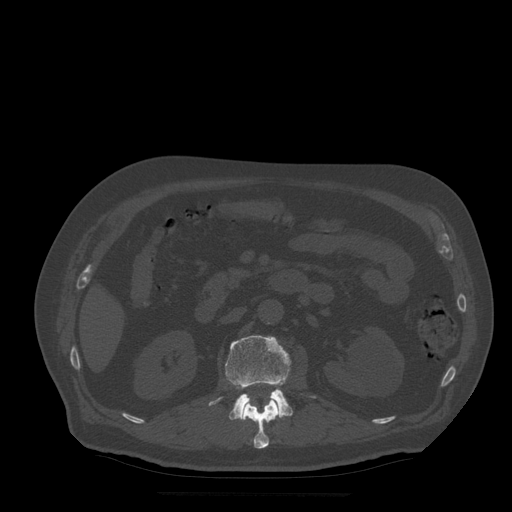
CT including the spine, one axial slice; slice 180 of 522 in the series (ordered by position); bone window (W 1800 / L 400 HU); 1.25 mm slice thickness; 512 × 512 image matrix, field of view 420 × 420 mm. Patient age 72 years. Case-level facts recorded for this patient, not image findings: primary cancer: prostate.
Annotated regions visible in this slice (semi-automatic segmentation, software-assisted and operator-edited):
- L1 vertebra: bounding box <242,385,280,449> (left, top, right, bottom; pixels)
- L2 vertebra: <209,336,315,420>